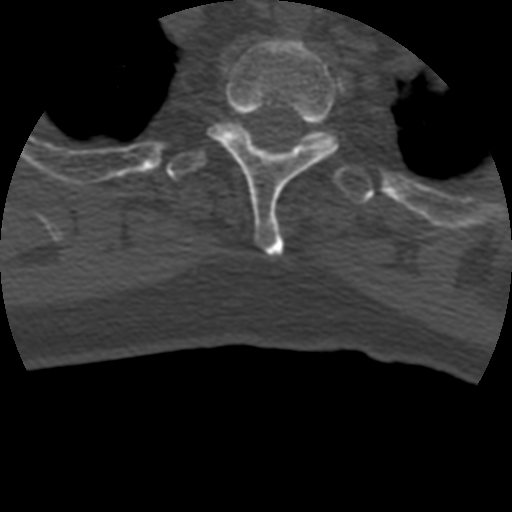
CT including the spine, one axial slice. Position 365 of 399 along the scan axis. Bone window (W 1800 / L 400 HU). 1.25 mm slice thickness. 512 × 512 image matrix. Patient age 69 years. Case-level facts recorded for this patient, not image findings: primary cancer: prostate.
Outlined on this slice (semi-automatic segmentation, software-assisted and operator-edited):
- T2 vertebra: bounding box <208,39,340,258> (left, top, right, bottom; pixels)
- T3 vertebra: <167,121,375,205>